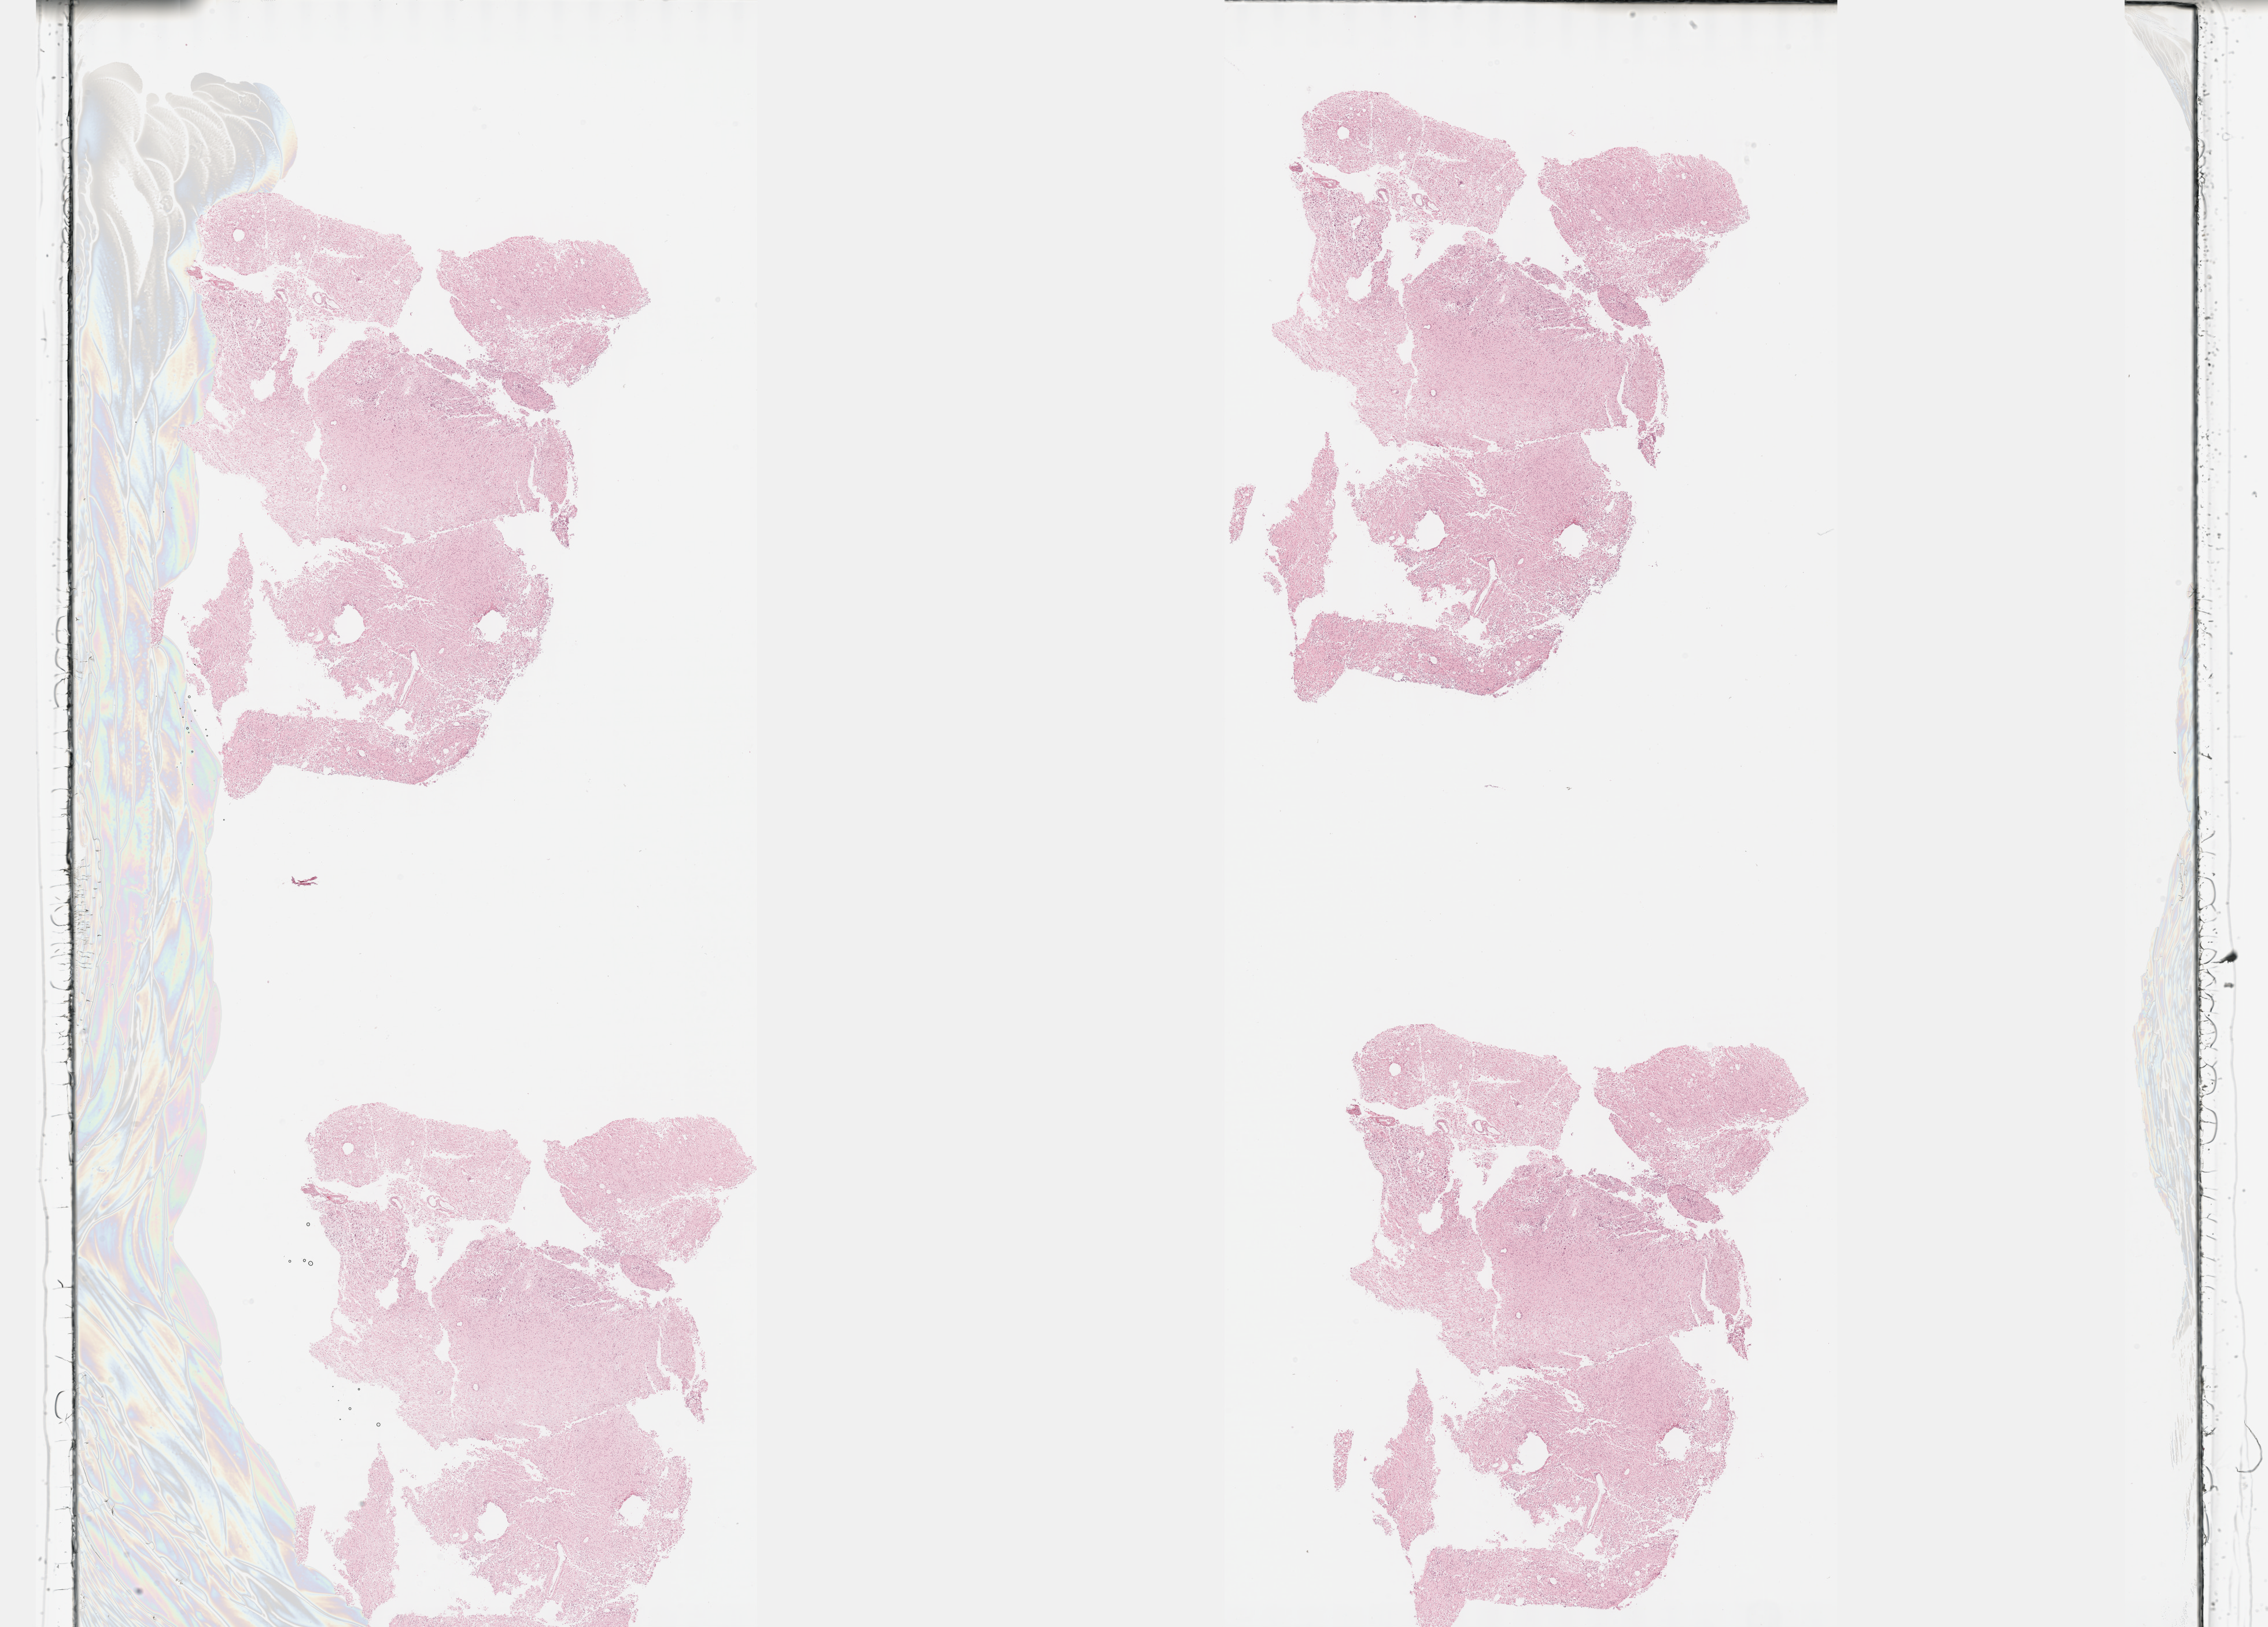
Digitized H&E-stained tissue section (whole slide) — low-resolution overview of the scanned area, about 31.7 x 22.7 mm (acquisition: 40x scan); formalin-fixed paraffin-embedded (FFPE) diagnostic section; sample: primary tumour, brain. Male, age 33 years at initial diagnosis. Histologic grade: G2 (moderately differentiated).
Histologic diagnosis: Astrocytoma, NOS (cerebrum).